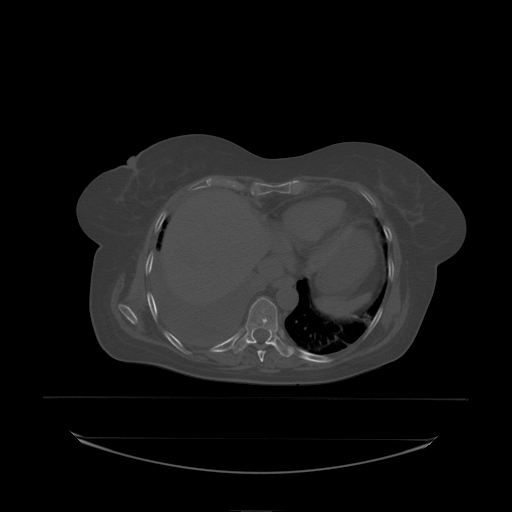
CT including the spine, one axial slice. Slice 126 of 242 in the series (ordered by position). Bone window (W 1800 / L 400 HU). 2.5 mm slice thickness. 512 × 512 image matrix, field of view 500 × 500 mm. Patient: female, 53 years. From the clinical record (not read from this slice): primary cancer: lung.
Outlined on this slice (semi-automatically segmented with operator editing):
- T9 vertebra: box from (x=245, y=298) to (x=278, y=338) px